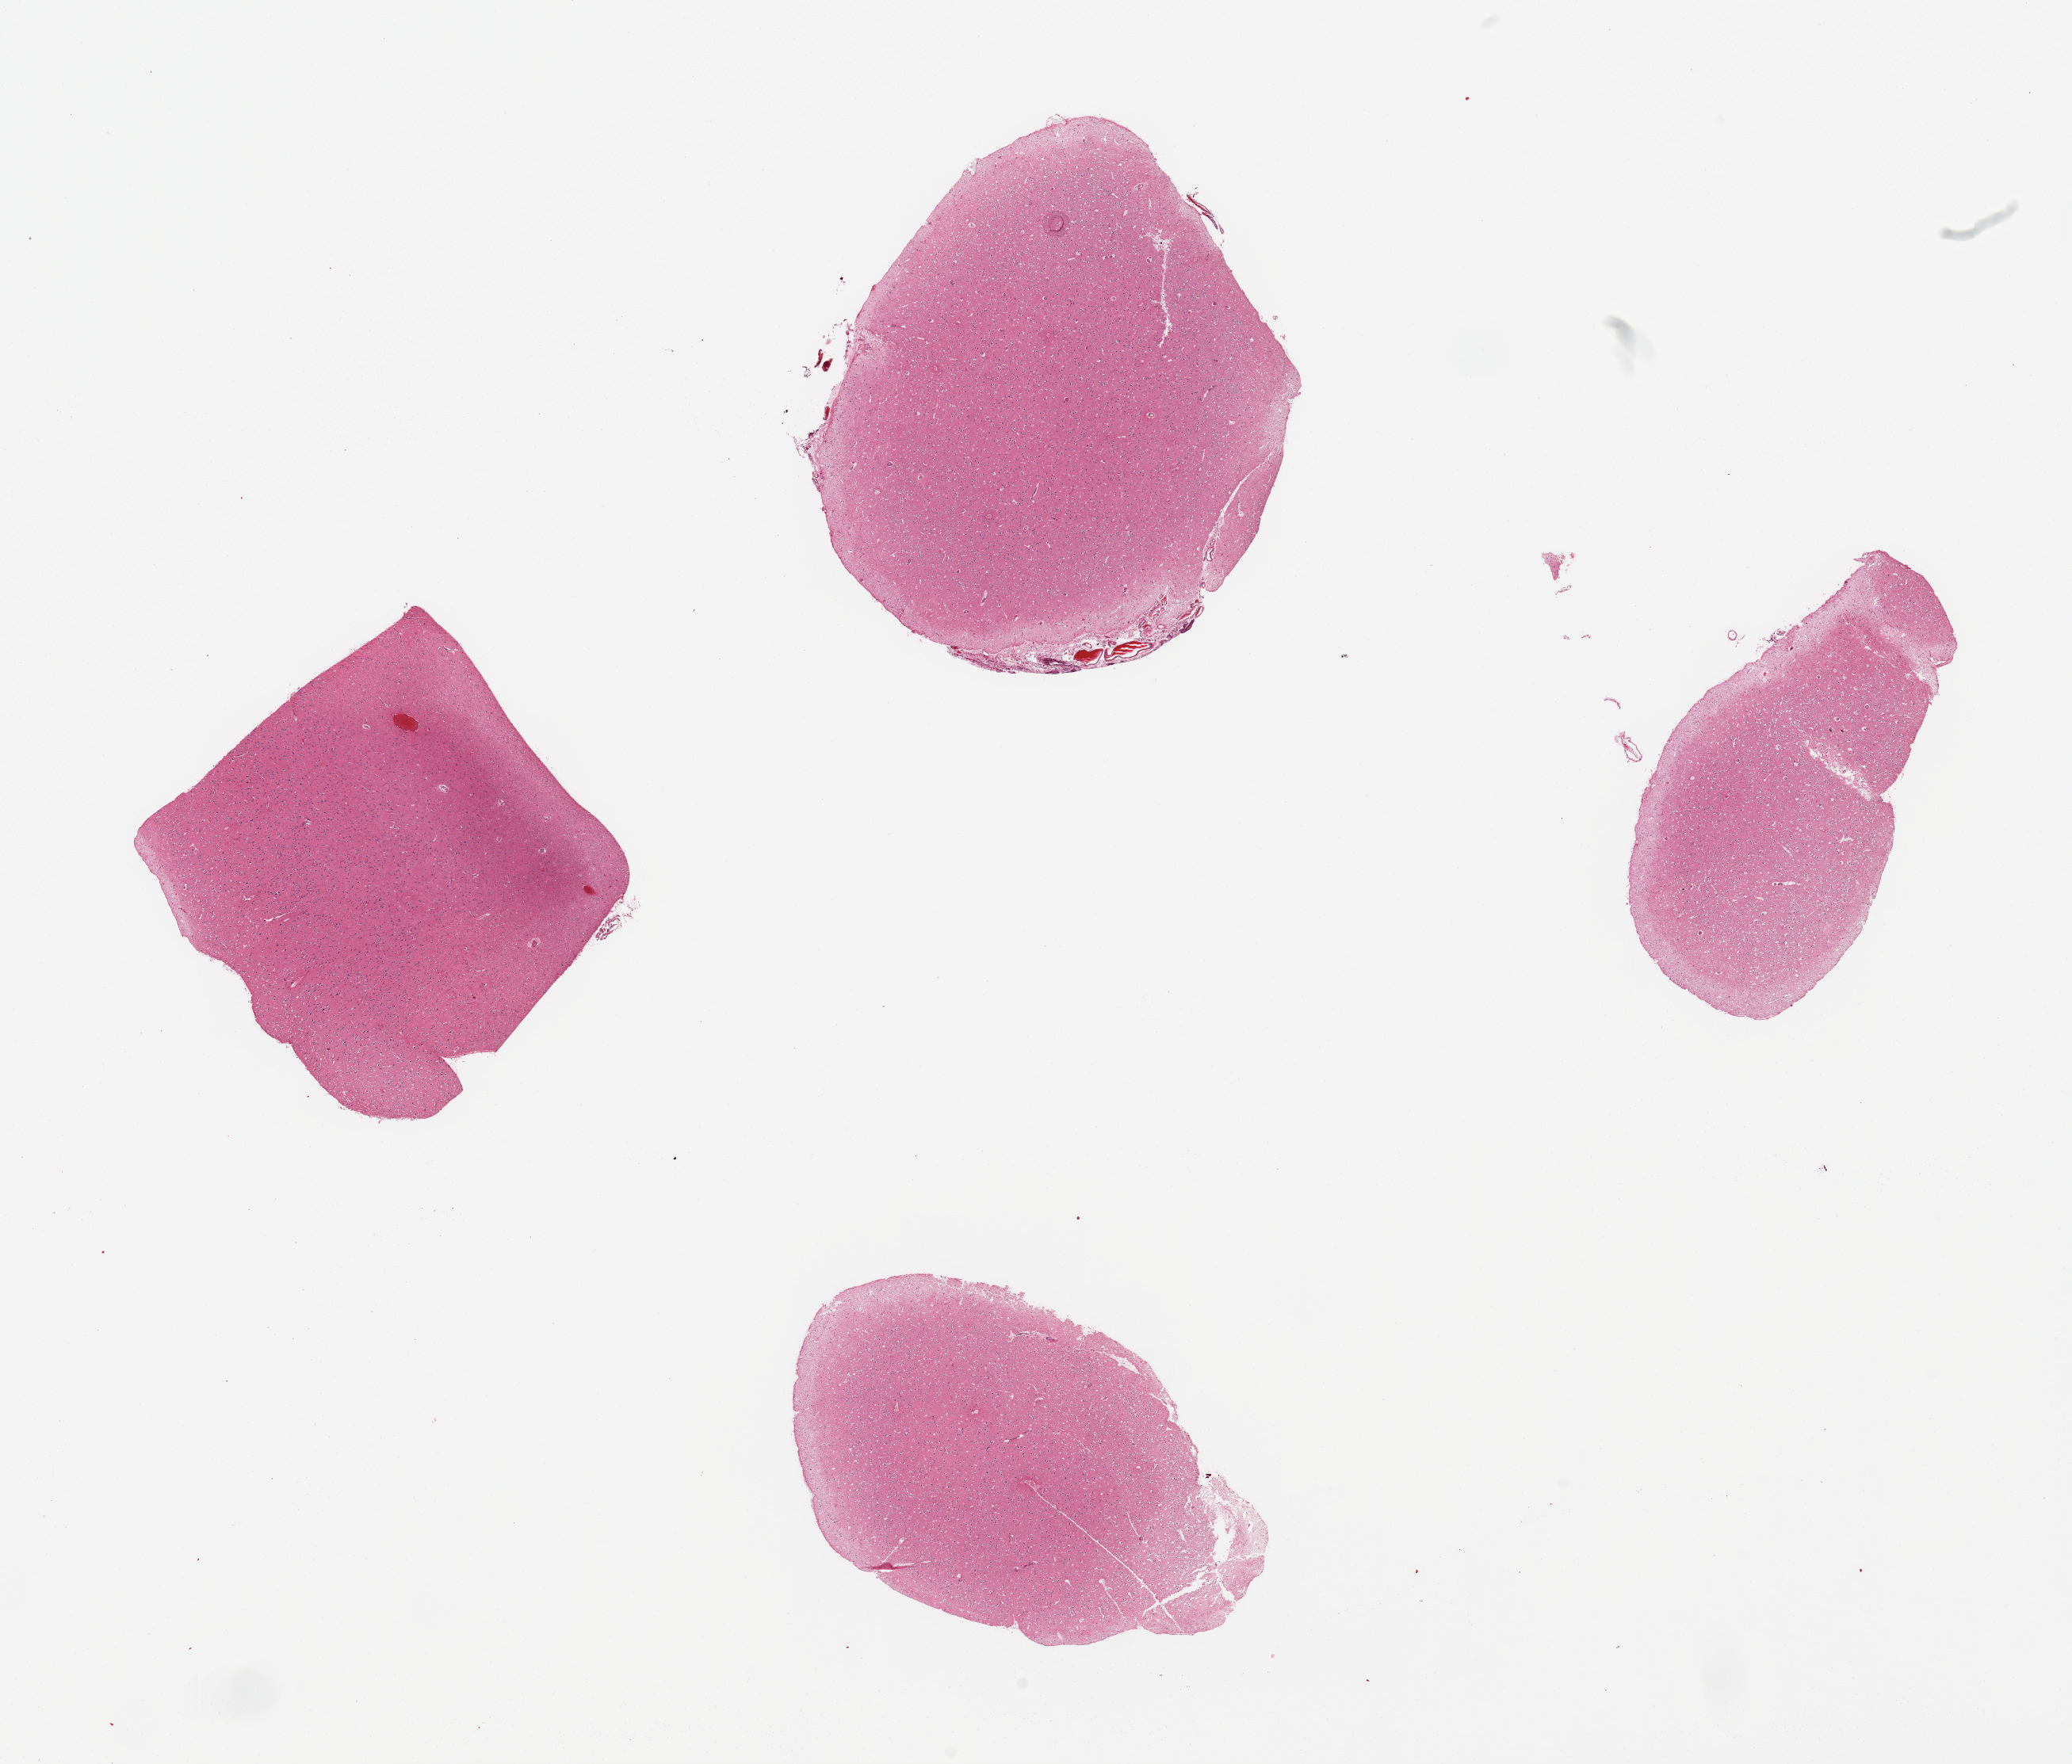
H&E whole-slide image, brightfield — low-resolution overview of the scanned area, about 20.7 x 17.6 mm (from a 20x scan). PAXgene-fixed paraffin-embedded (PFPE) section. Sampled site (target tissue): cerebral cortex. Tissue donor sample. Donor: female.
Pathologist's review note for this sample: 4 pieces, some attached meninges.